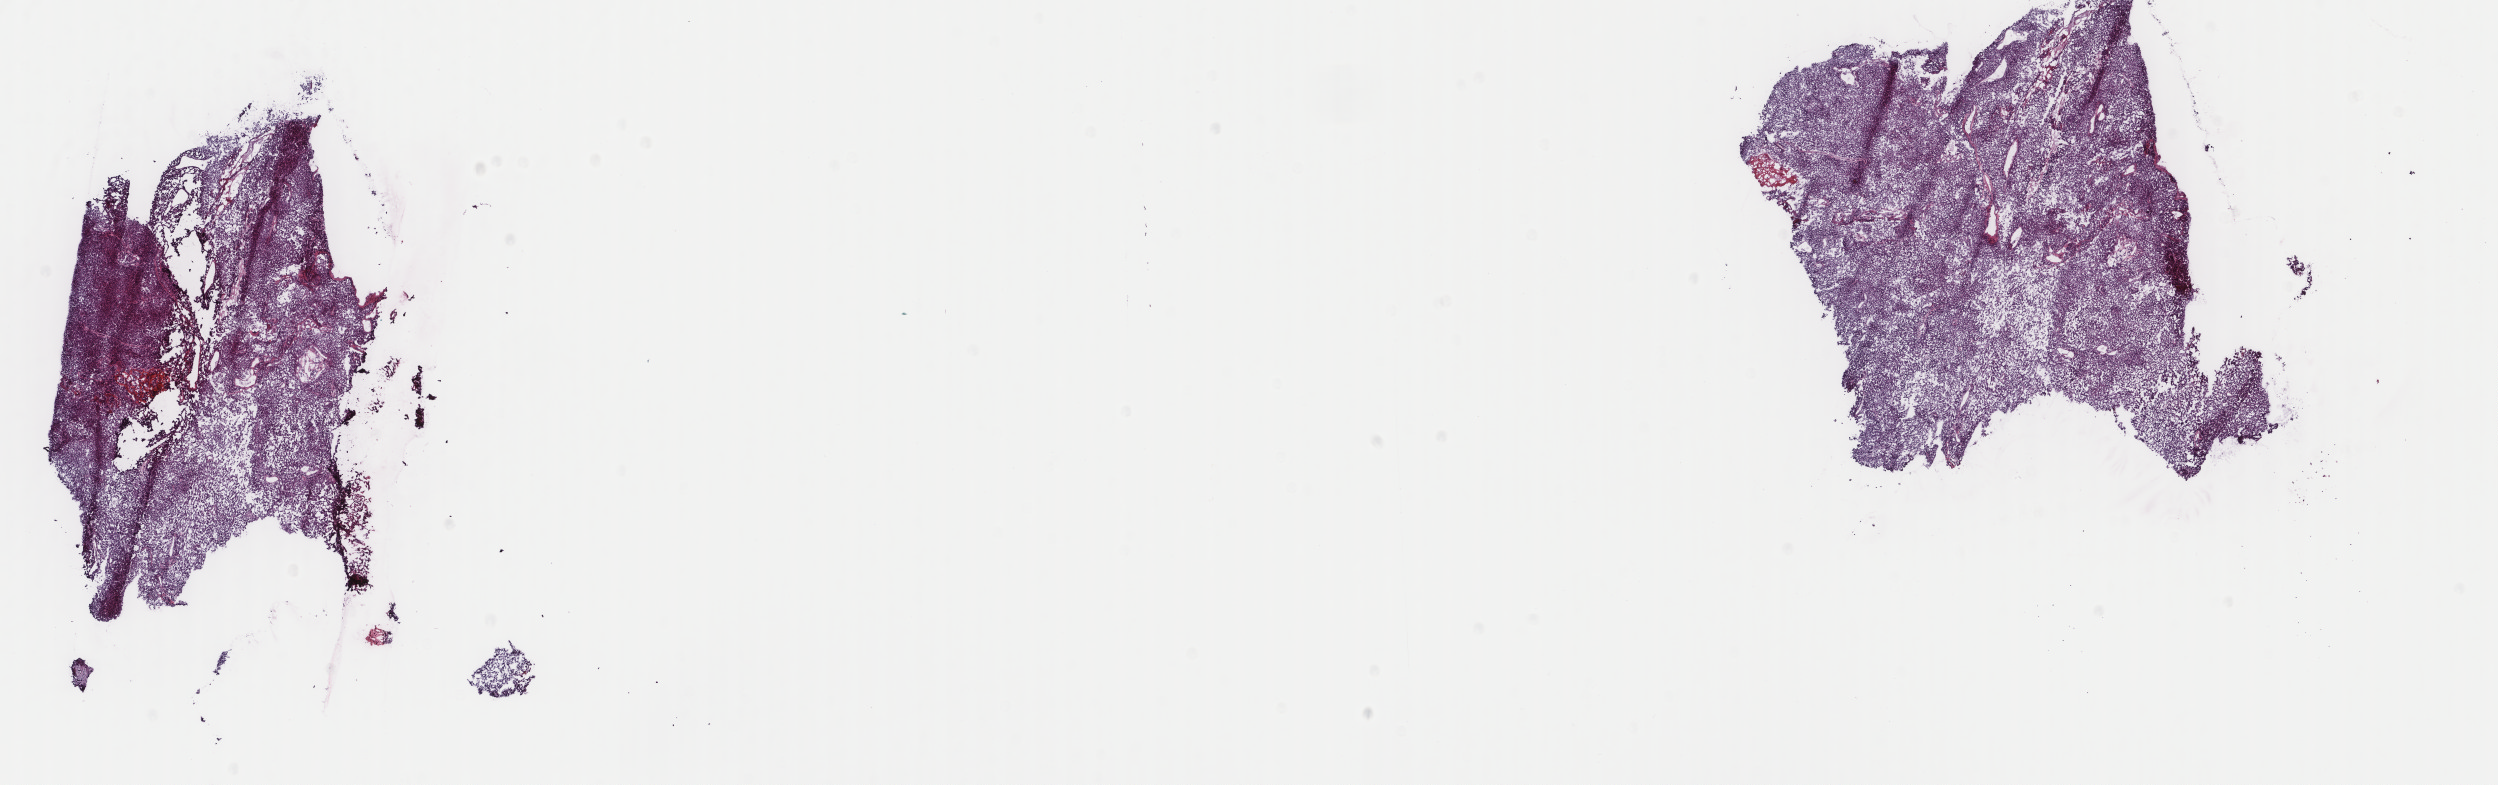
Whole-slide histology image, Hematoxylin and eosin (H&E) stained — whole scanned area (about 19.8 x 6.2 mm, acquisition: 40x scan) shown as a low-resolution overview, frozen section from the top of the tissue portion, metastatic tumour sample, sampled site: spinal cord. Patient: female, age at initial diagnosis 66 years. Slide review estimates, as recorded: tumour cells 98%, tumour nuclei 80%, normal cells 0%, stromal cells 0%, necrosis 2%. Inflammatory infiltration, as recorded: lymphocyte infiltration 1%, monocyte infiltration 1%, neutrophil infiltration 0%.
- this section: metastatic tumour tissue
- patient diagnosis: Malignant melanoma, NOS